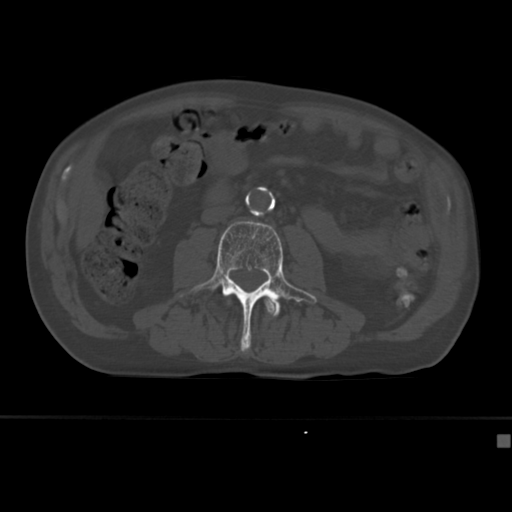
CT including the spine, one axial slice. 120 kVp. Bone window (W 1800 / L 400 HU). 1.5 mm slice thickness. 512 × 512 image matrix, field of view 337 × 337 mm. Patient: male, 64 years. From the clinical record (not read from this slice): primary cancer: uterus.
Structures marked on this image (semi-automatically segmented with operator editing):
- L2 vertebra: bounding box <228,298,276,312> (left, top, right, bottom; pixels)
- L3 vertebra: <179,221,317,353>